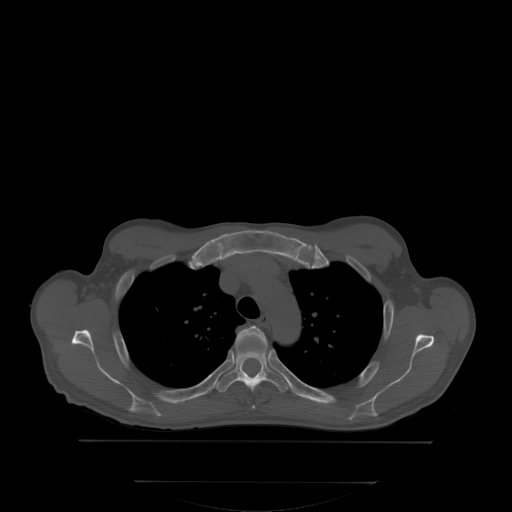
CT including the spine, one axial slice. Slice 261 of 350 in the series (ordered by position). Bone window (W 1800 / L 400 HU). 2.5 mm slice thickness. 512 × 512 image matrix. Male patient, age 58 years. Case-level facts recorded for this patient, not image findings: primary cancer: prostate; vertebrae with lytic lesions (as recorded): L1.
Annotated regions visible in this slice (semi-automatically segmented with operator editing):
- T3 vertebra: bounding box <240,325,264,341> (left, top, right, bottom; pixels)
- T4 vertebra: <216,337,287,391>